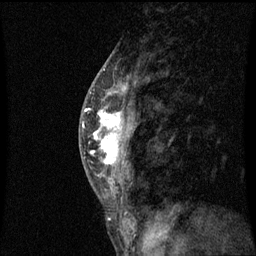
Breast MRI (dynamic contrast-enhanced), one sagittal slice. Position 33 of 60 along the scan axis. Dynamic contrast-enhanced series, image 2 of 3 at this slice position (ordered by acquisition). 1.5 T. TE 4.2 ms, TR 8.9 ms. 2 mm slice thickness. 256 × 256 image matrix. Female patient, age 50 years. Case-level facts recorded for this patient, not image findings: setting: breast cancer imaged before/during neoadjuvant chemotherapy; receptor status: triple-negative.
Annotated regions visible in this slice (semi-automatically segmented with operator editing):
- analysis volume of interest (the breast-tissue region the enhancement analysis was run in; not a lesion): bounding box (x1, y1, x2, y2) in pixels: (84, 80, 139, 171)
- tumour enhancement mask (voxels above the 70 % enhancement threshold inside the analysis volume of interest): (84, 88, 125, 165)